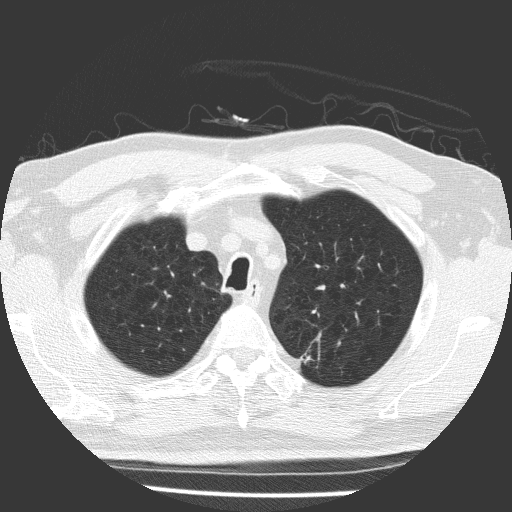
Chest CT (low-dose screening protocol), one axial image; first (baseline) screen; lung window (W 1500 / L -600 HU); 2 mm slice thickness; 120 kVp; slice 33 of 169 in the series. Male, age 64 years at enrolment. Former smoker at enrolment.
Expert reader's lesion annotation, box from (x=284, y=341) to (x=327, y=380) px. The exam's reader record, not a measurement of the box and not confirmed to be the same lesion: non-calcified nodule or mass ≥4 mm, left upper lobe, 9 × 7 mm, spiculated (stellate) margins, soft tissue attenuation. Official screen result: positive, change unspecified: nodule(s) >= 4 mm or enlarging nodule(s), mass(es), or other non-specific abnormalities suspicious for lung cancer. Participant outcome: lung cancer diagnosed 70 days after this screen — adenocarcinoma, NOS, left upper lobe, poorly differentiated (G3), stage IIA (AJCC 6th edition), 9 mm at pathology.